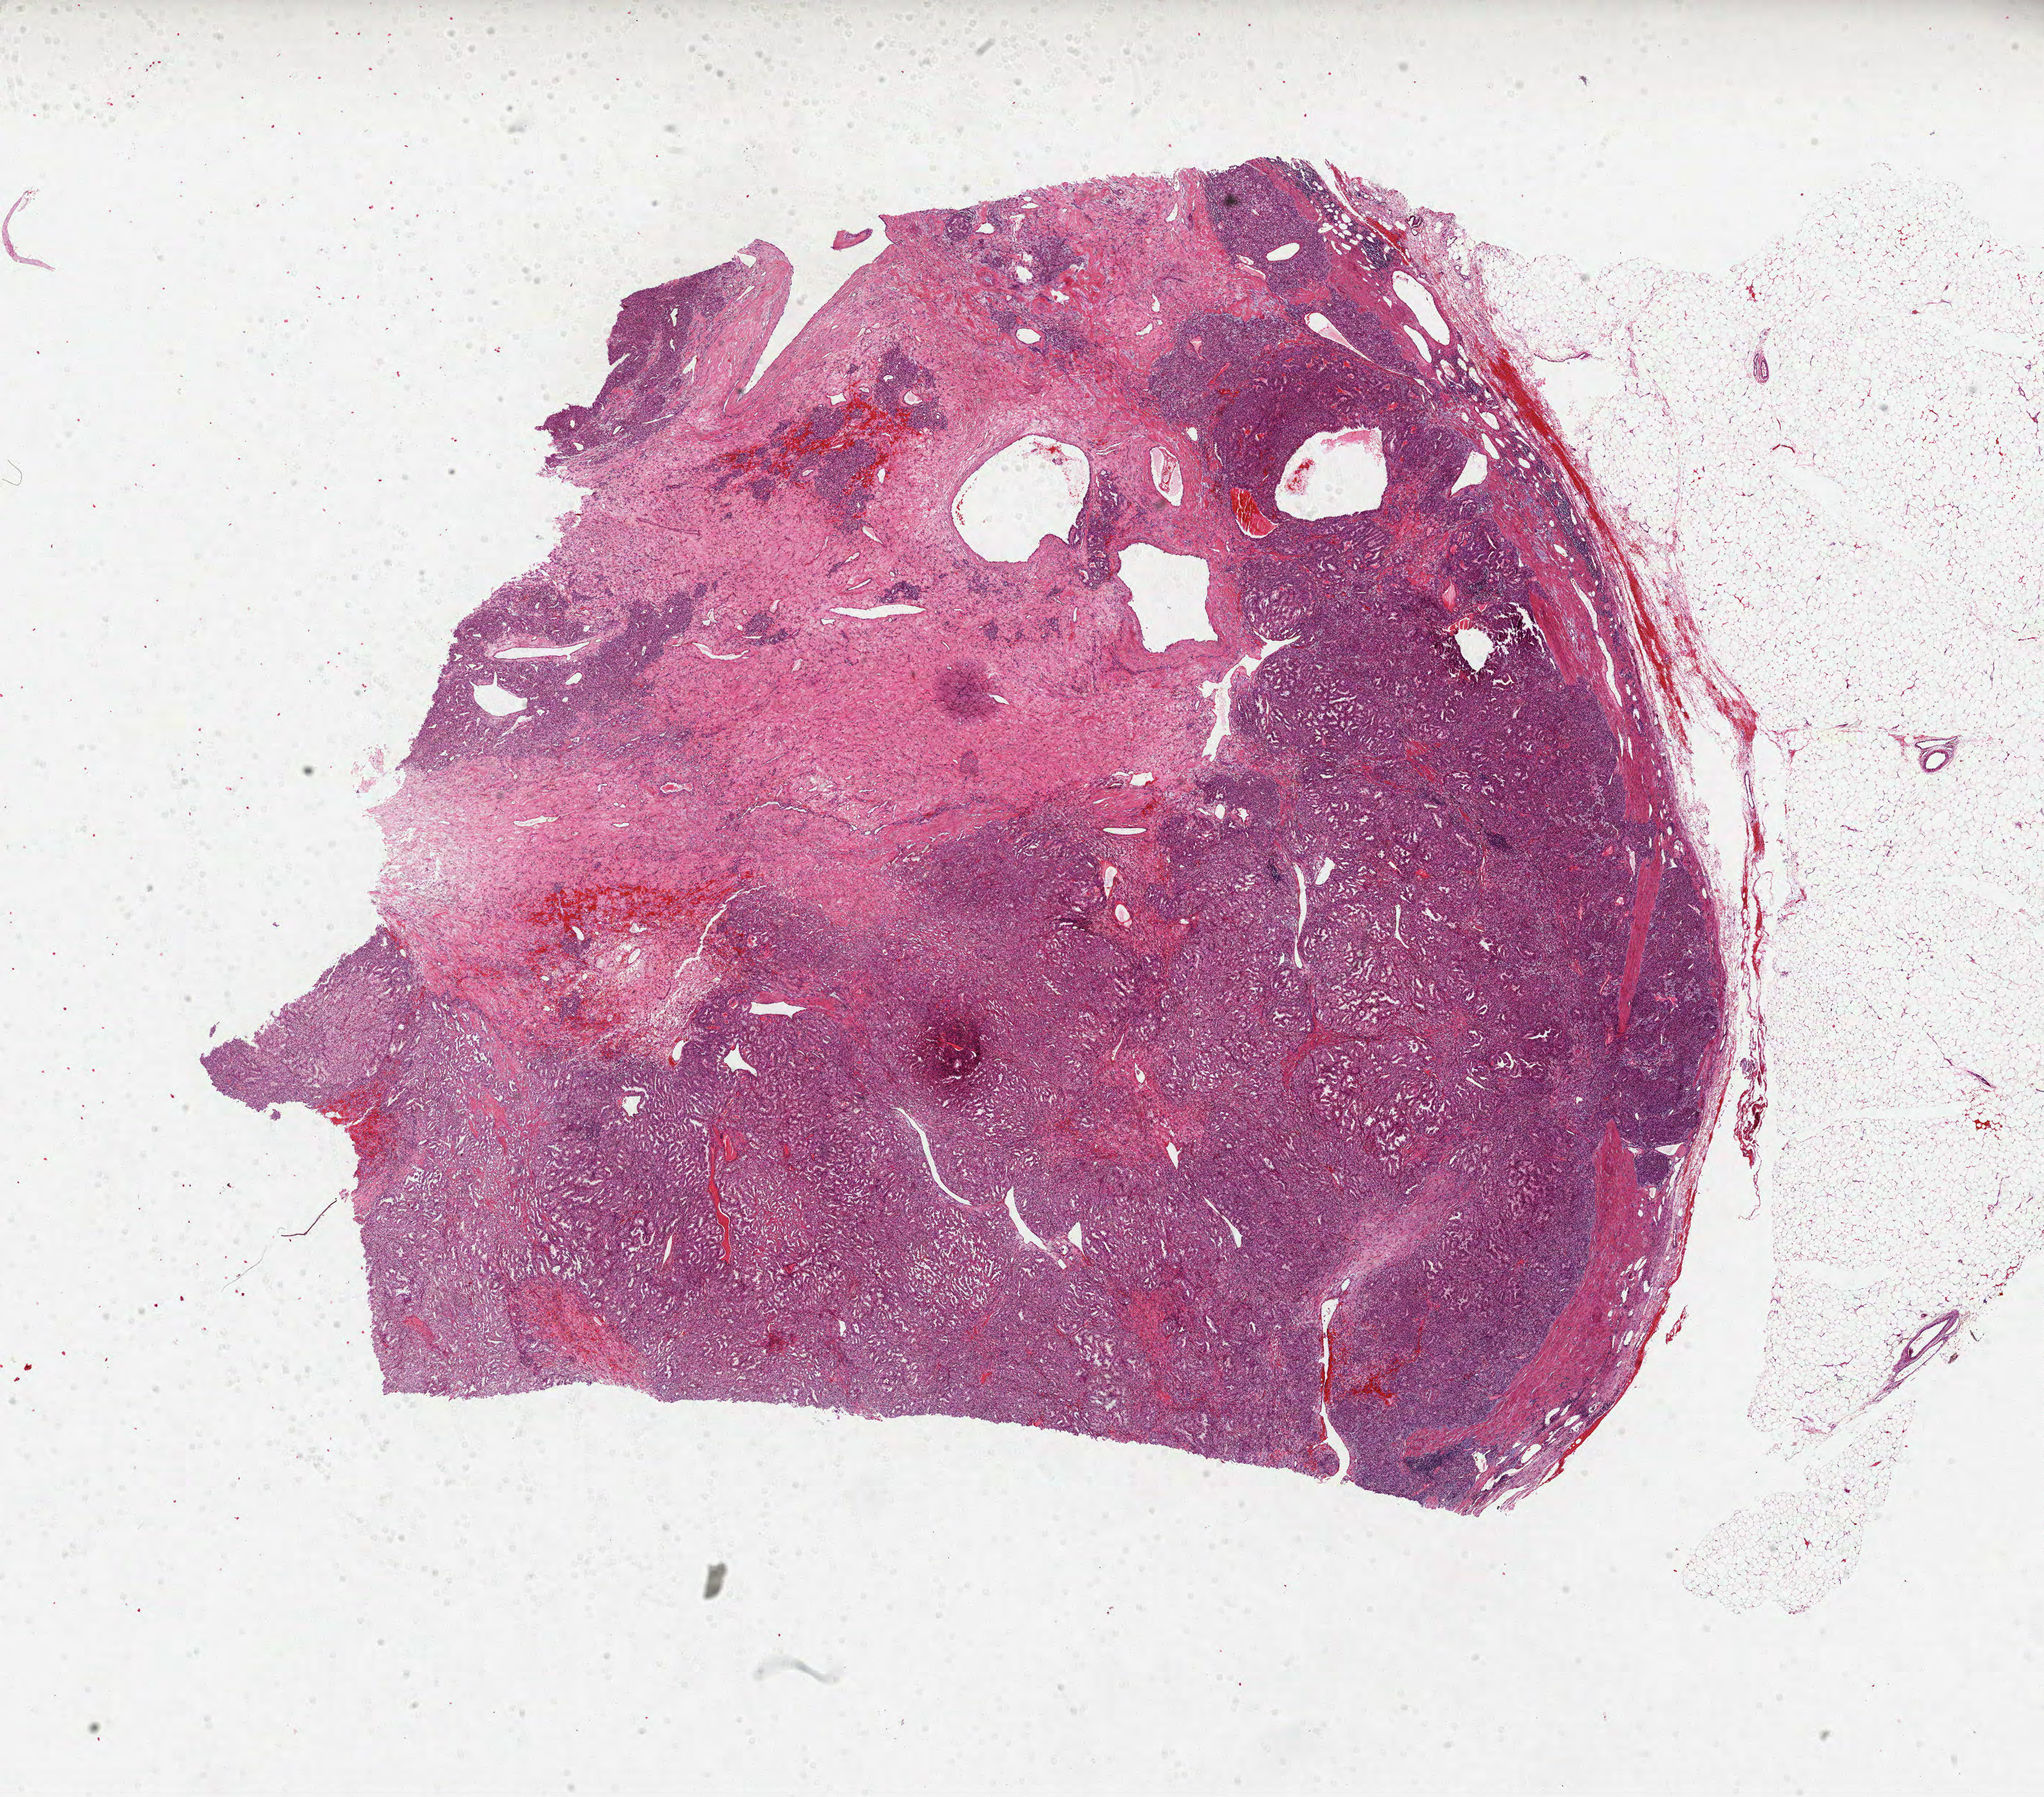
H&E whole-slide image, shown as a low-resolution overview of the whole scanned area (about 22.7 x 20.0 mm, slide scanned at 40x); formalin-fixed paraffin-embedded (FFPE) diagnostic section; kidney, primary tumour sample. Female patient; age at initial diagnosis 74 years.
Diagnosis: Papillary adenocarcinoma, NOS. AJCC pathologic stage: I (7th edition).